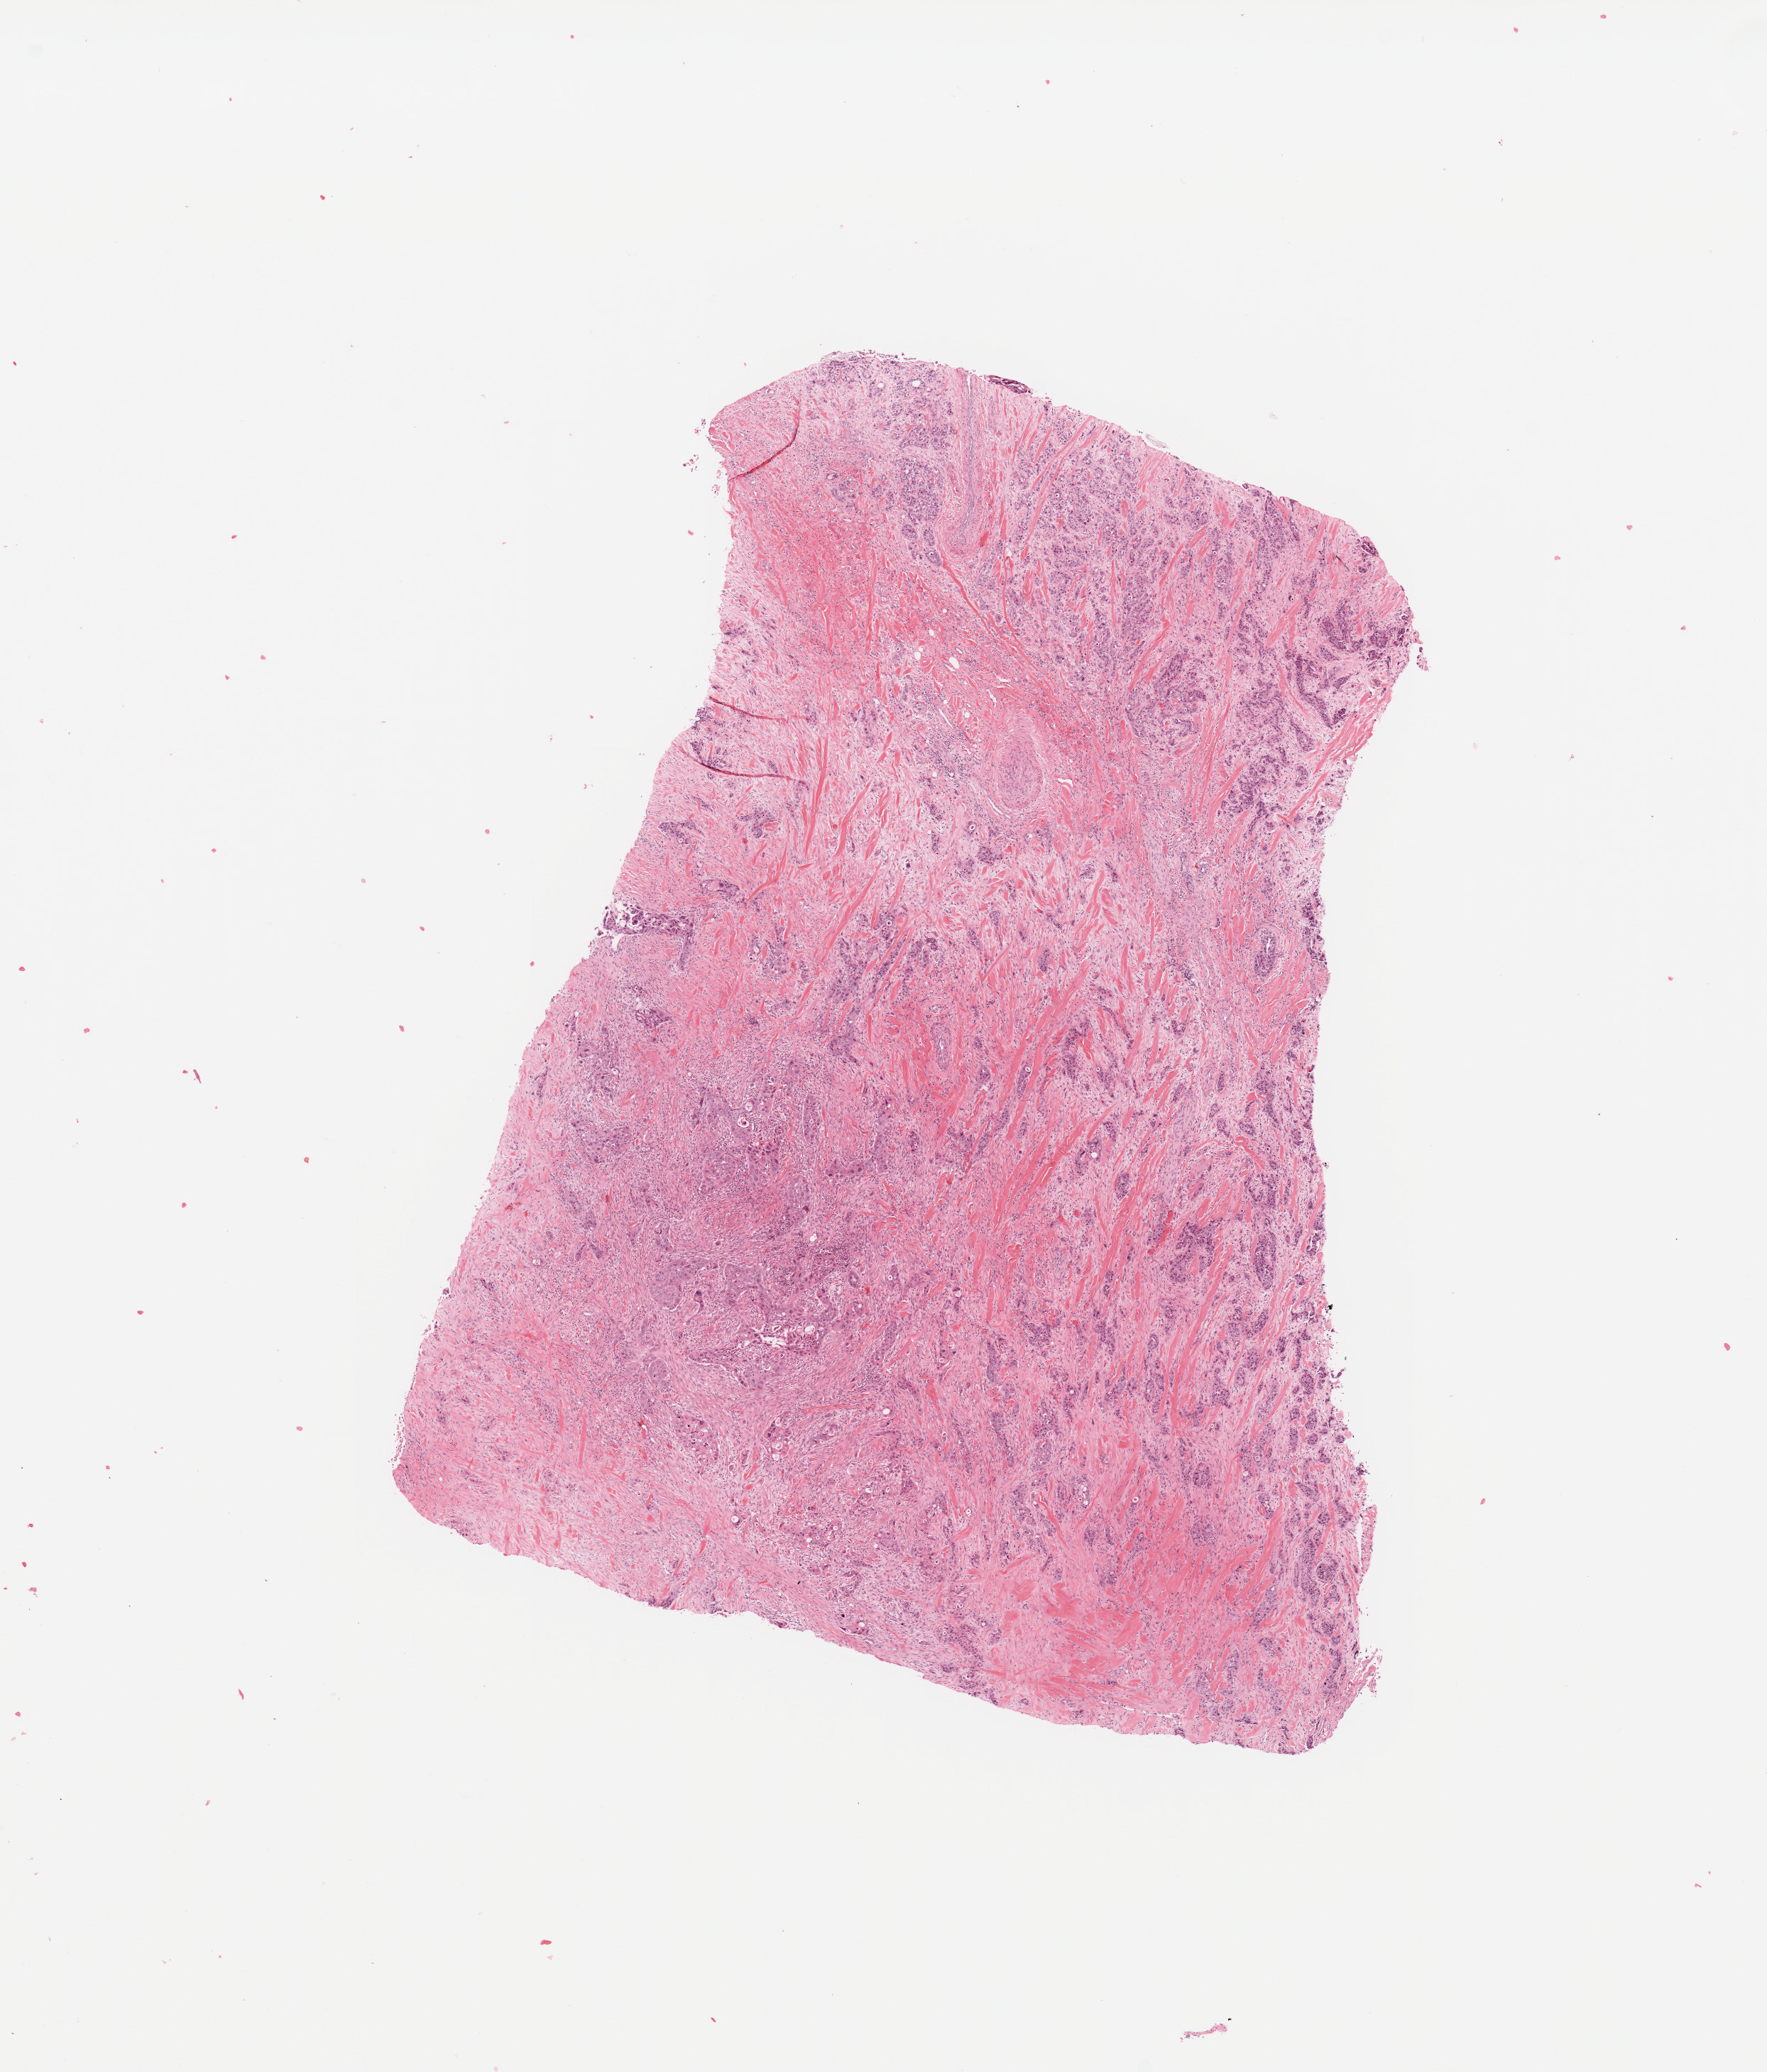
Whole-slide histology image, H&E, shown as a low-resolution overview of the whole scanned area (about 9.8 x 11.5 mm, slide scanned at 20x). Tumour tissue sample, sampled site: lung. Male, 40 y/o. Histologic grade: G3 (poorly differentiated). Slide review estimates, as recorded: tumour nuclei 60%, necrosis 5%.
* AJCC pathologic stage: IIIA
* histologic diagnosis: Squamous cell carcinoma, NOS
* primary tumour site (as recorded): right middle lobe